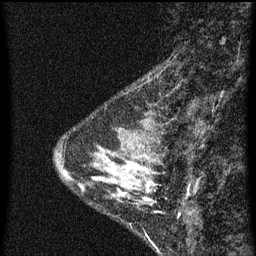
Breast MRI (dynamic contrast-enhanced), one sagittal slice; position 20 of 60 along the scan axis; dynamic contrast-enhanced series, image 2 of 3 at this slice position (ordered by acquisition); 1.5 T; TE 4.2 ms, TR 8 ms; 2 mm slice thickness; 256 × 256 image matrix. Patient: female, 34 years.
Outlined on this slice (semi-automatically segmented with operator editing):
- analysis volume of interest (the breast-tissue region the enhancement analysis was run in; not a lesion): bounding box <70,138,155,201> (left, top, right, bottom; pixels)
- tumour enhancement mask (voxels above the 70 % enhancement threshold inside the analysis volume of interest): <146,186,149,201>